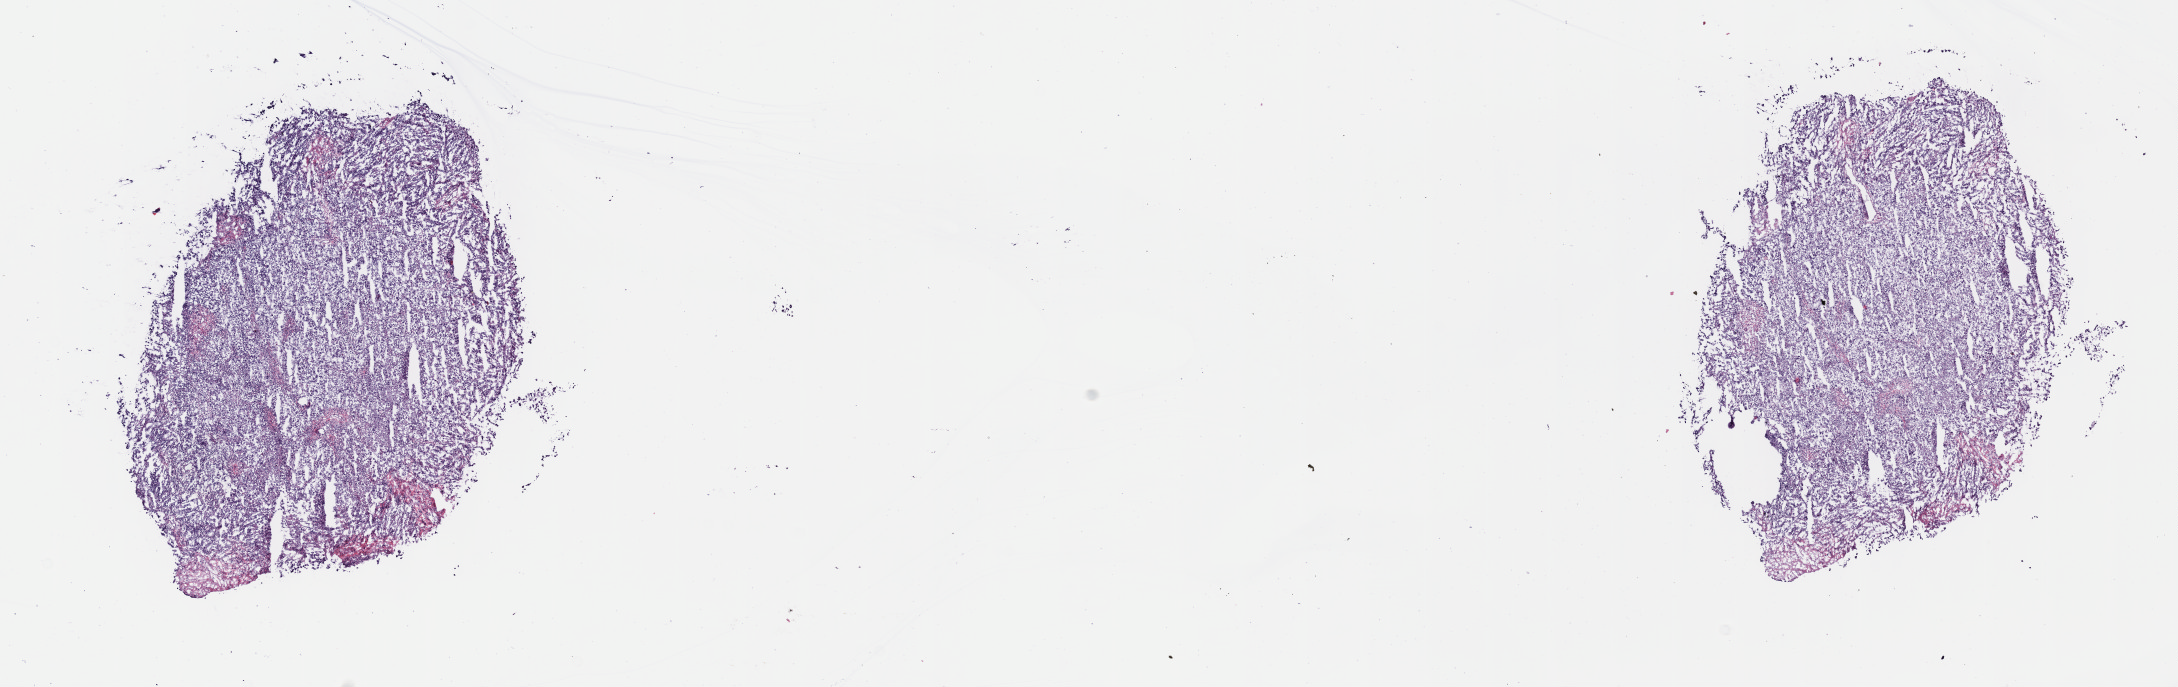
Digitized H&E-stained tissue section (whole slide), whole scanned area (about 17.6 x 5.6 mm, from a 40x scan) shown as a low-resolution overview, frozen section from the top of the tissue portion, testis, primary tumour sample. Male, age 49 years at initial diagnosis. Pathologist review of this section (percent, as recorded): tumour cells 90%, tumour nuclei 95%, normal cells 0%, stromal cells 10%, necrosis 0%. Inflammatory infiltration, as recorded: lymphocyte infiltration 0%, monocyte infiltration 0%, neutrophil infiltration 0%.
Laterality: left. Histologic diagnosis: Seminoma, NOS. AJCC pathologic stage: I (7th edition).